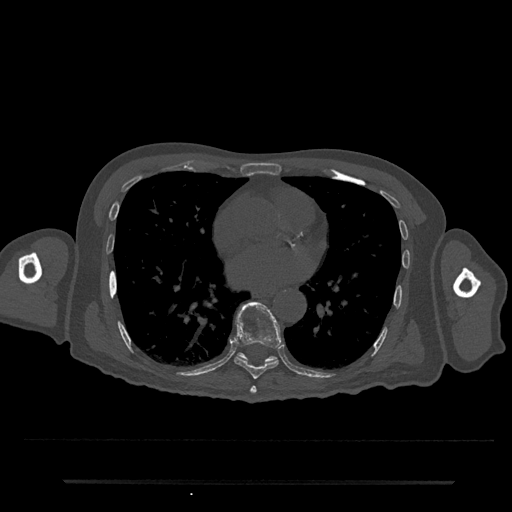
CT including the spine, one axial slice. Slice 409 of 797 in the series (ordered by position). Bone window (W 1800 / L 400 HU). 0.5 mm slice thickness. 512 × 512 image matrix, field of view 427 × 427 mm. Male patient, age 74 years. Case-level facts recorded for this patient, not image findings: primary cancer: prostate.
Annotated regions visible in this slice (semi-automatic segmentation, software-assisted and operator-edited):
- T7 vertebra: bounding box <250,386,257,394> (left, top, right, bottom; pixels)
- T8 vertebra: <234,302,282,379>
- T9 vertebra: <238,352,276,362>